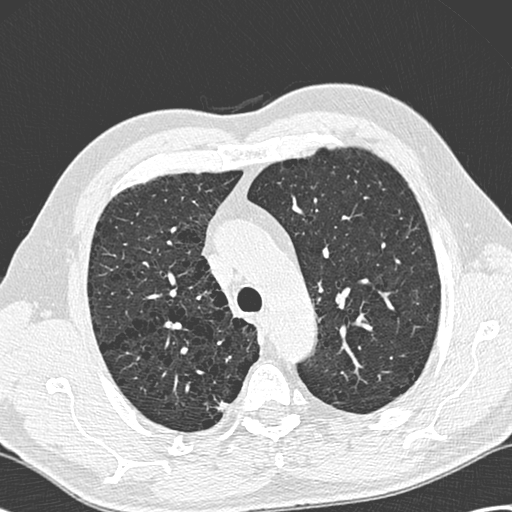
Chest CT (low-dose screening protocol), one axial image. First (baseline) screen. Lung window (W 1500 / L -600 HU). Lung (sharp) reconstruction kernel (D). Slice 64 of 258 in the series. 512 × 512 image matrix. Male participant, aged 68 years at enrolment.
• Expert-annotated lung lesion, bounding box (x1, y1, x2, y2) in pixels: (205, 392, 241, 421).
• No non-calcified nodule or mass ≥4 mm was recorded by the screening reader at this exam.
• Official screen result: negative screen, minor abnormalities not suspicious for lung cancer.
• Later outcome: lung cancer diagnosed 777 days after this screen — adenocarcinoma, NOS, right upper lobe, well differentiated (G1), stage IB (AJCC 6th edition), 15 mm at pathology.